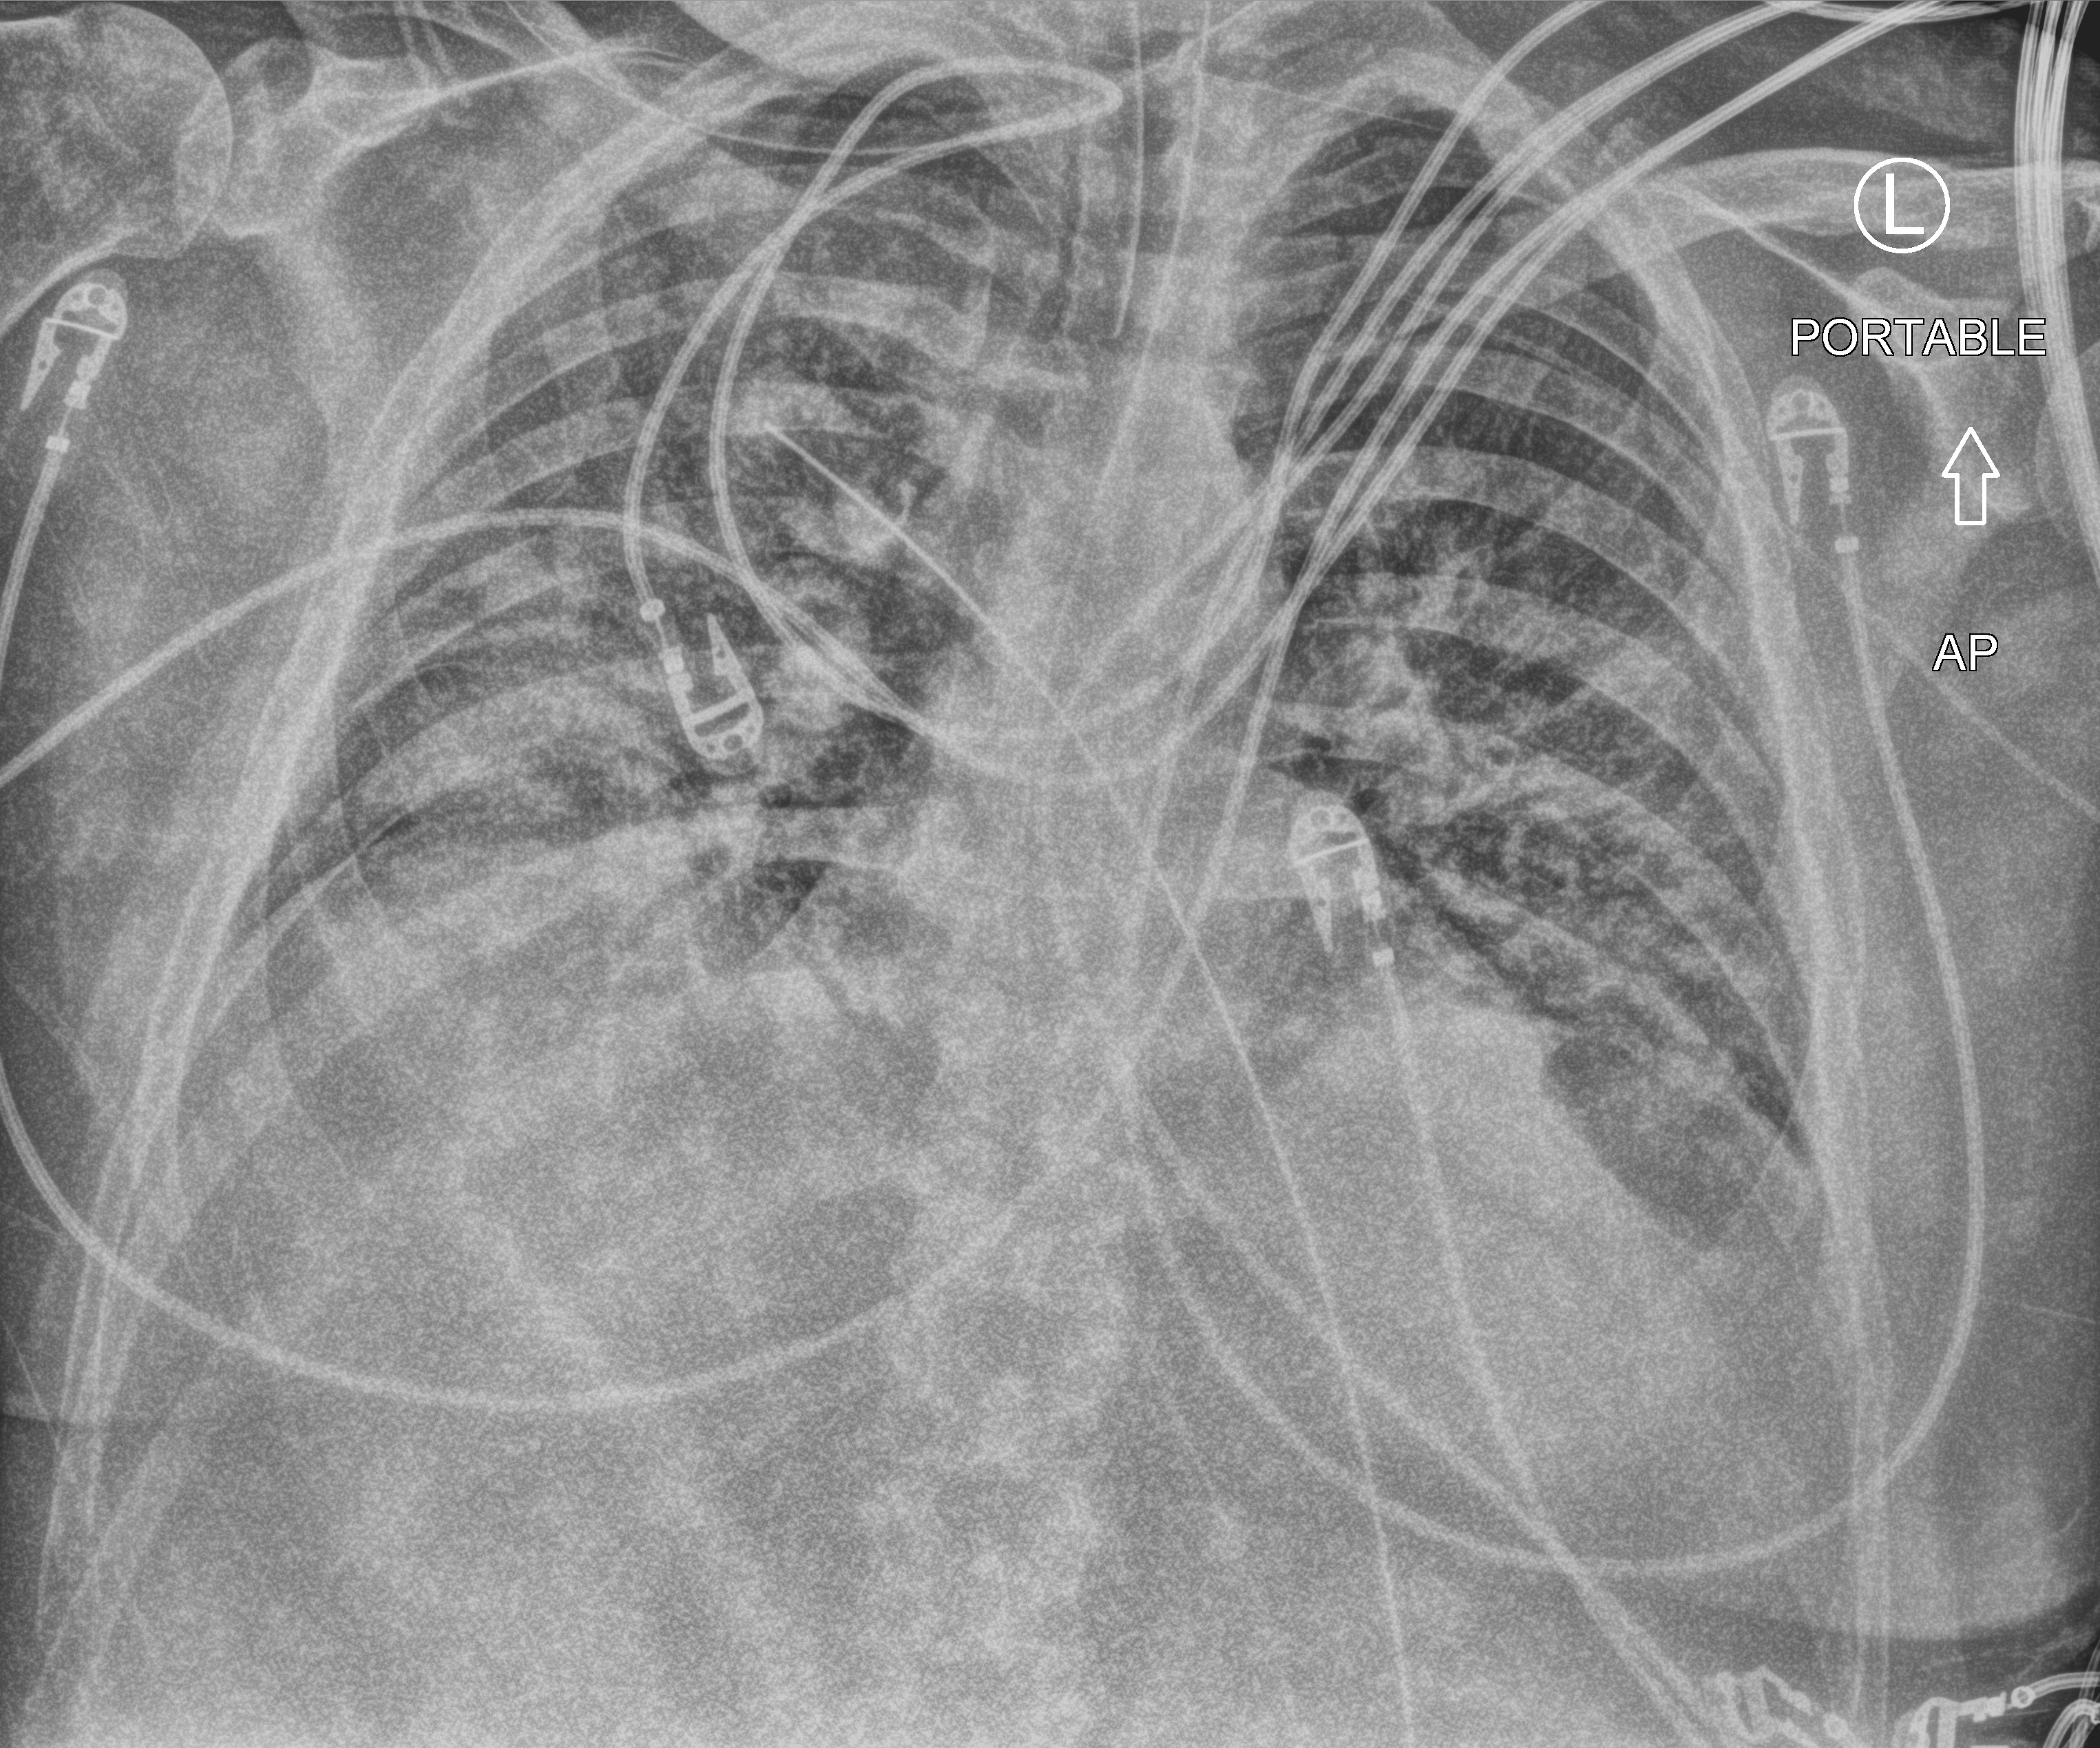
Bedside chest radiograph (computed radiography); anteroposterior (AP) projection. Patient hospitalised with COVID-19; male, aged 18–59 years.
From the hospital-stay record, not from the radiograph (when in the stay this image was taken is not recorded): admitted to intensive care during this hospital stay: yes.